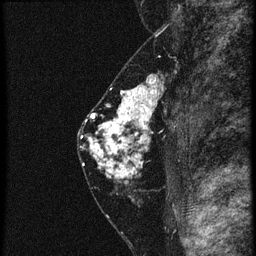
Breast MRI (dynamic contrast-enhanced), one sagittal slice; position 34 of 60 along the scan axis; 4 images stored at this slice position (order not interpretable as contrast timing); 1.5 T; TE 4.2 ms, TR 20.4 ms; 256 × 256 image matrix, field of view 180 × 180 mm. Female patient, age 46 years. Case-level facts recorded for this patient, not image findings: setting: breast cancer imaged before/during neoadjuvant chemotherapy; receptor status: triple-negative.
Outlined on this slice (semi-automatically segmented with operator editing):
- analysis volume of interest (the breast-tissue region the enhancement analysis was run in; not a lesion): bounding box <88,82,177,185> (left, top, right, bottom; pixels)
- tumour enhancement mask (voxels above the 90 % enhancement threshold inside the analysis volume of interest): <88,82,163,179>